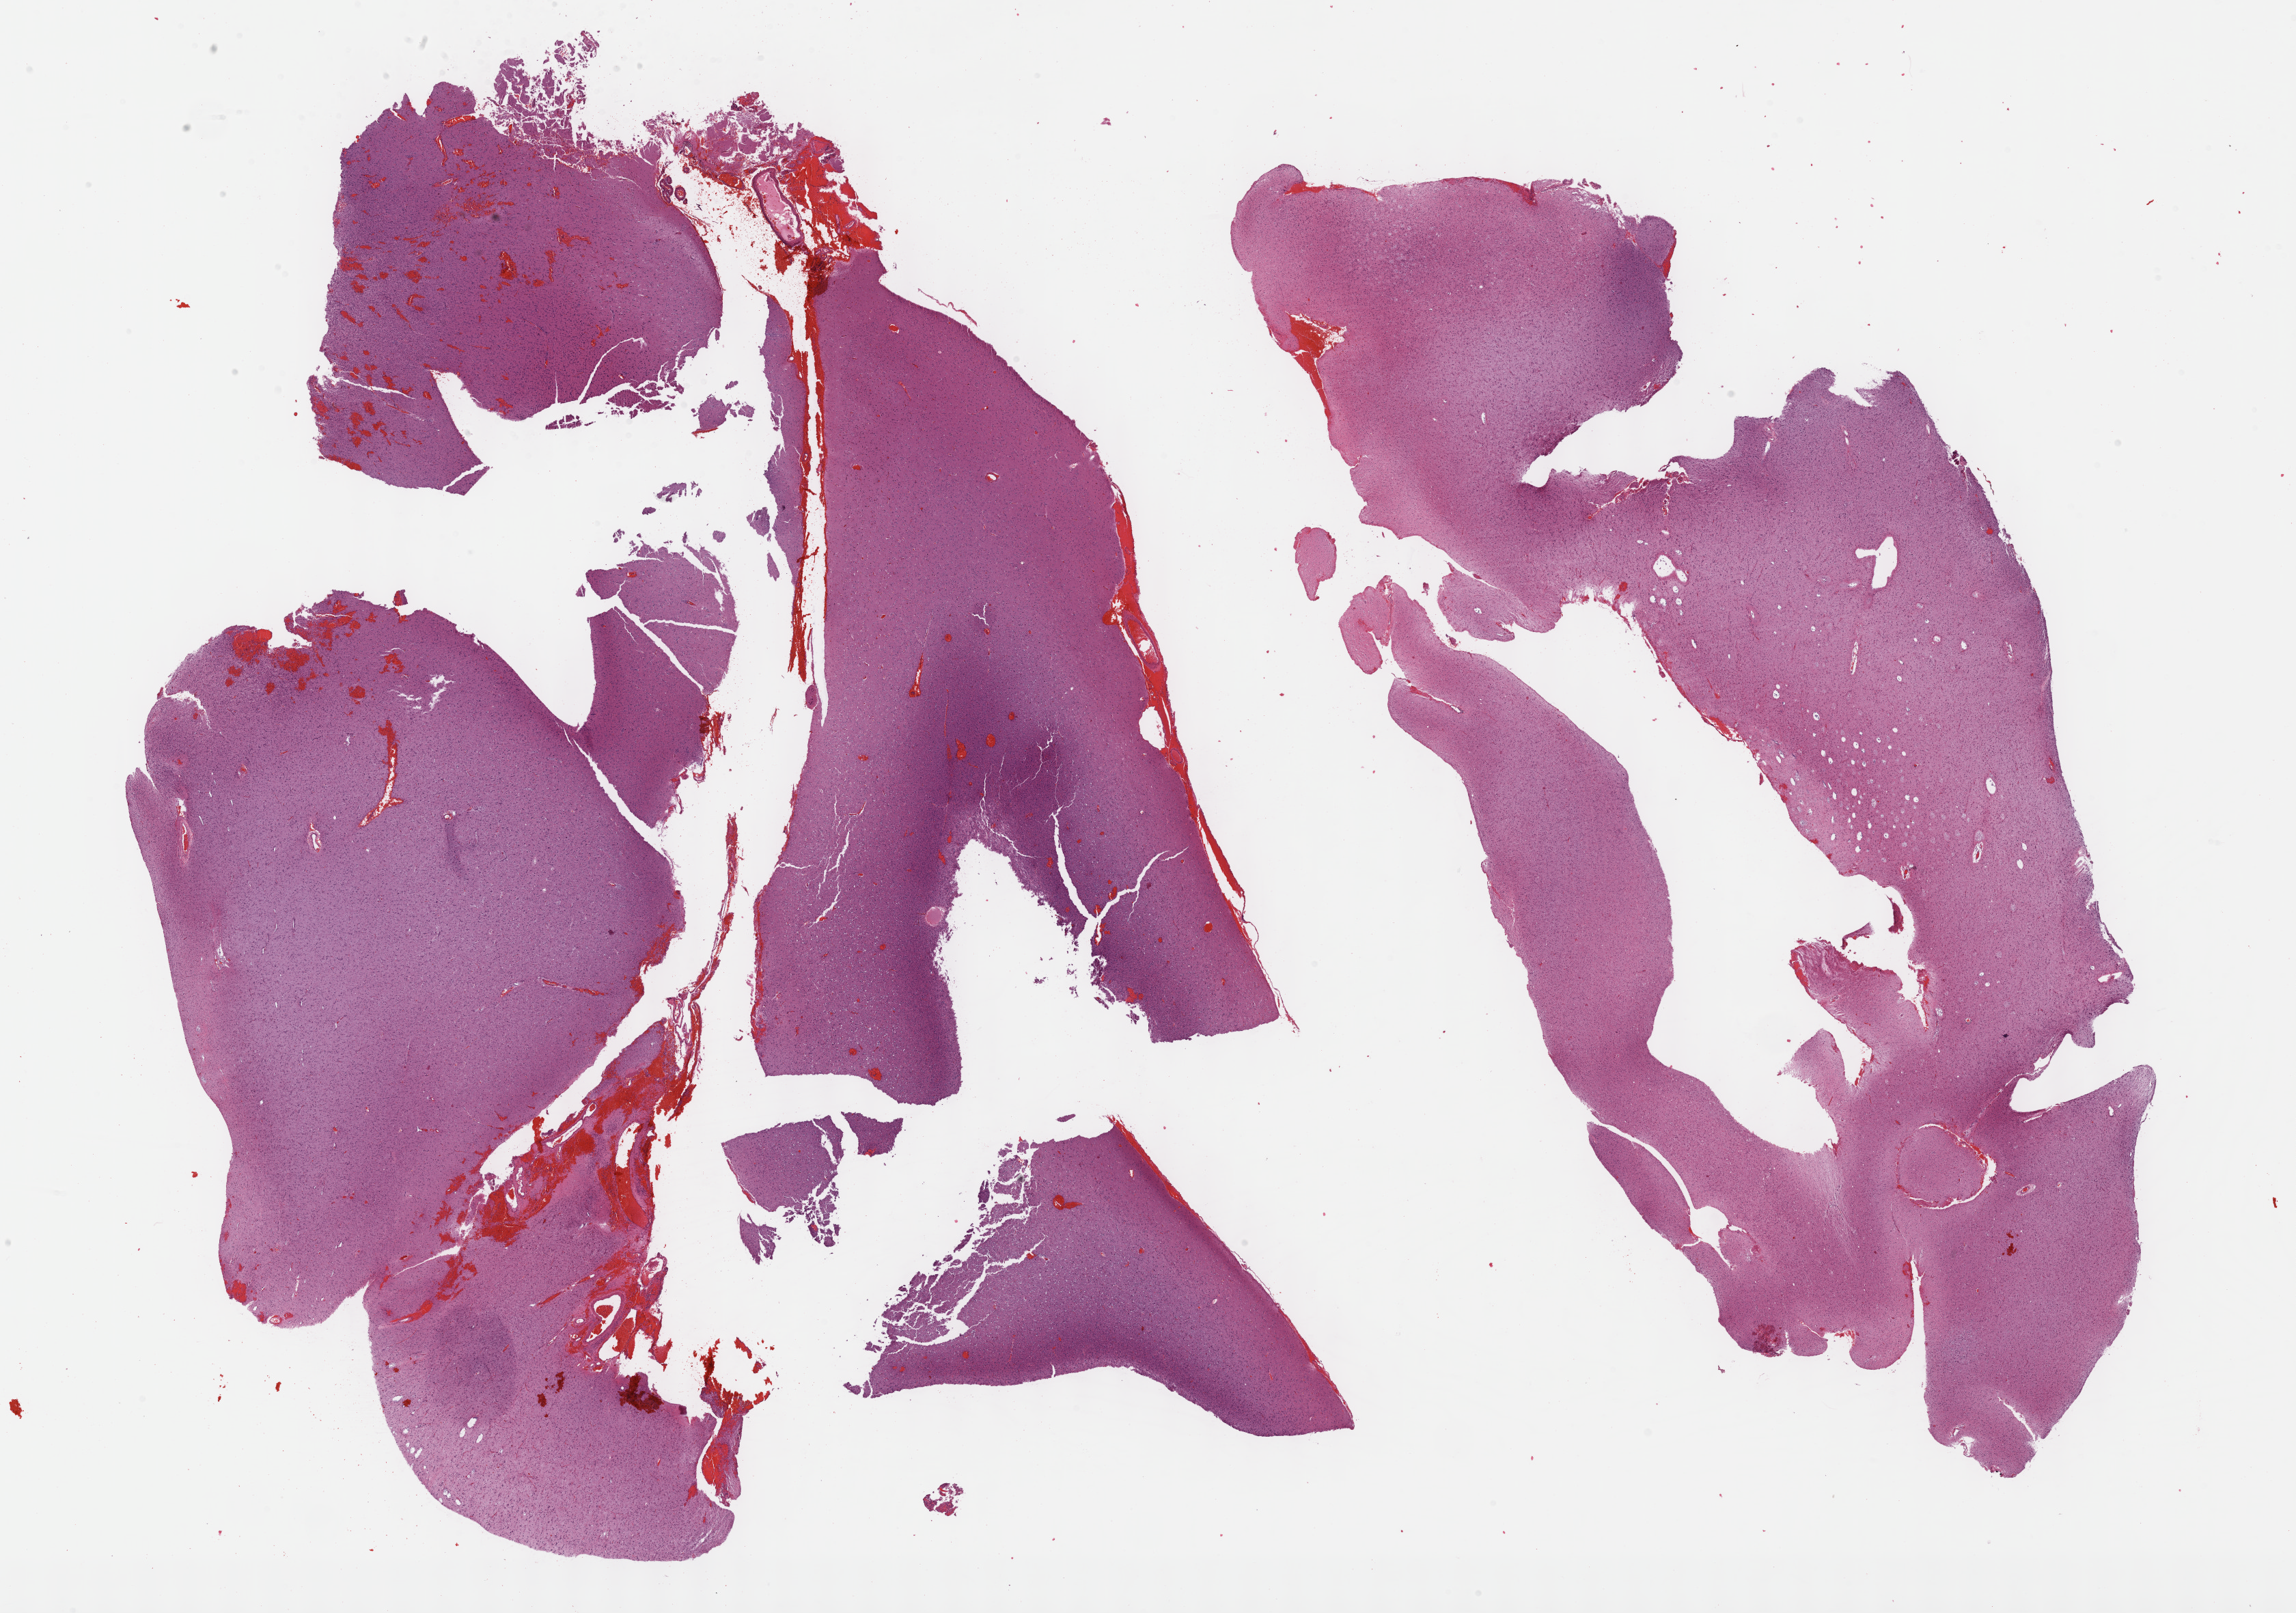
Digitized H&E tissue section (whole slide), shown as a low-resolution overview of the whole scanned area (about 27.2 x 19.1 mm). Formalin-fixed paraffin-embedded (FFPE) diagnostic section. Sample: primary tumour, brain. Male, age 29 years at initial diagnosis. Histologic grade: G2 (moderately differentiated).
- histologic diagnosis: Oligodendroglioma, NOS